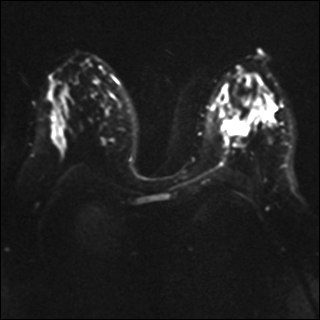
Breast MRI, one axial slice; slice 21 of 37 in the series (ordered by position); diffusion-weighted series; image 2 of 4 stored at this slice position (different b-values; order by instance number); 1.5 T; 320 × 320 image matrix, field of view 340 × 340 mm. Female patient.
Outlined on this slice (manually delineated by an expert):
- tumour on diffusion-weighted imaging: bounding box [x1, y1, x2, y2] px = [222, 118, 251, 135]